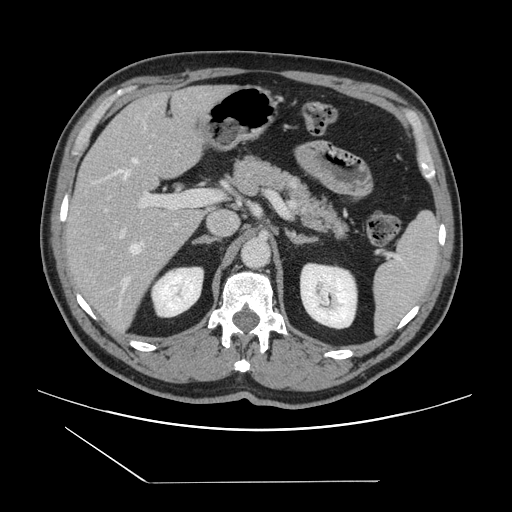
Contrast-enhanced abdominal CT, one axial slice; slice 84 of 157 in the series (ordered by position); 120 kVp; intravenous contrast given; soft-tissue window (W 400 / L 40 HU); 2.5 mm slice thickness; 512 × 512 image matrix, field of view 407 × 407 mm. Male patient, age 61 years. Case-level facts recorded for this patient, not image findings: diagnosis: colorectal cancer liver metastases, imaged before liver resection; multiple liver metastases: yes; largest metastasis: 5.5 cm; disease in both lobes: yes.
Outlined on this slice (outlined manually by an expert reader):
- hepatic veins: bounding box (x1, y1, x2, y2) in pixels: (119, 158, 143, 288)
- liver: (66, 86, 228, 336)
- planned liver remnant (the part of the liver to remain after resection): (67, 86, 228, 221)
- portal vein (with intrahepatic branches): (105, 190, 206, 305)